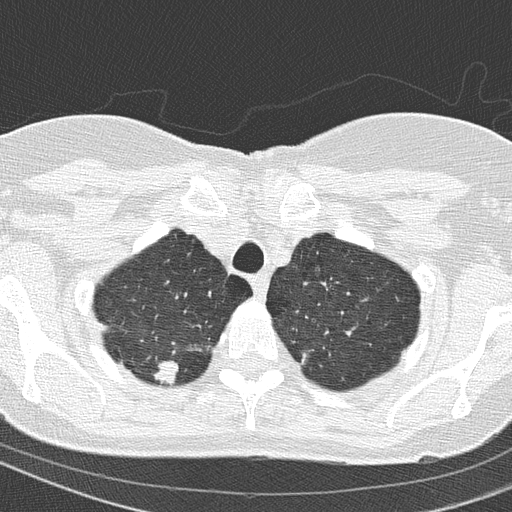
Axial slice from a low-dose chest CT screening exam. Baseline screening round. Lung window (W 1500 / L -600 HU). 2 mm slice thickness. 120 kVp. Slice 22 of 154 in the series. Female participant, aged 67 years at enrolment. Current smoker at enrolment.
Lesion marked by an expert reader, bounding box [x1, y1, x2, y2] px = [129, 343, 191, 392]. The exam's reader record, not a measurement of the box and not confirmed to be the same lesion: non-calcified nodule or mass ≥4 mm, right upper lobe, 15 × 14 mm, spiculated (stellate) margins, soft tissue attenuation. Official screen result: positive, change unspecified: nodule(s) >= 4 mm or enlarging nodule(s), mass(es), or other non-specific abnormalities suspicious for lung cancer. Lung cancer was diagnosed 63 days after this screen: adenocarcinoma, NOS, right upper lobe, moderately differentiated (G2), stage IA (AJCC 6th edition), 14 mm at pathology.